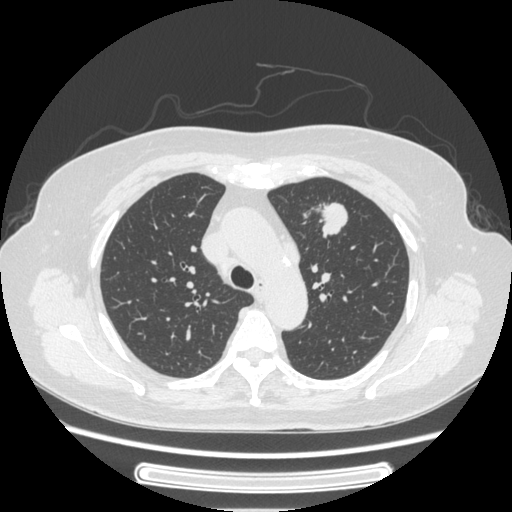
Chest CT, one axial slice; slice 172 of 227 in the series (ordered by position); lung window (W 1500 / L -600 HU); 1.25 mm slice thickness; 512 × 512 image matrix, field of view 363 × 363 mm. Female patient, age 77 years. From the clinical record (not read from this slice): clinical TNM (as recorded): T1c N3 M0; histopathological grade: G2-3.
Outlined on this slice (bounding box drawn by a radiologist):
- lung tumour (recorded histology: adenocarcinoma): bounding box <311,195,354,249> (left, top, right, bottom; pixels)